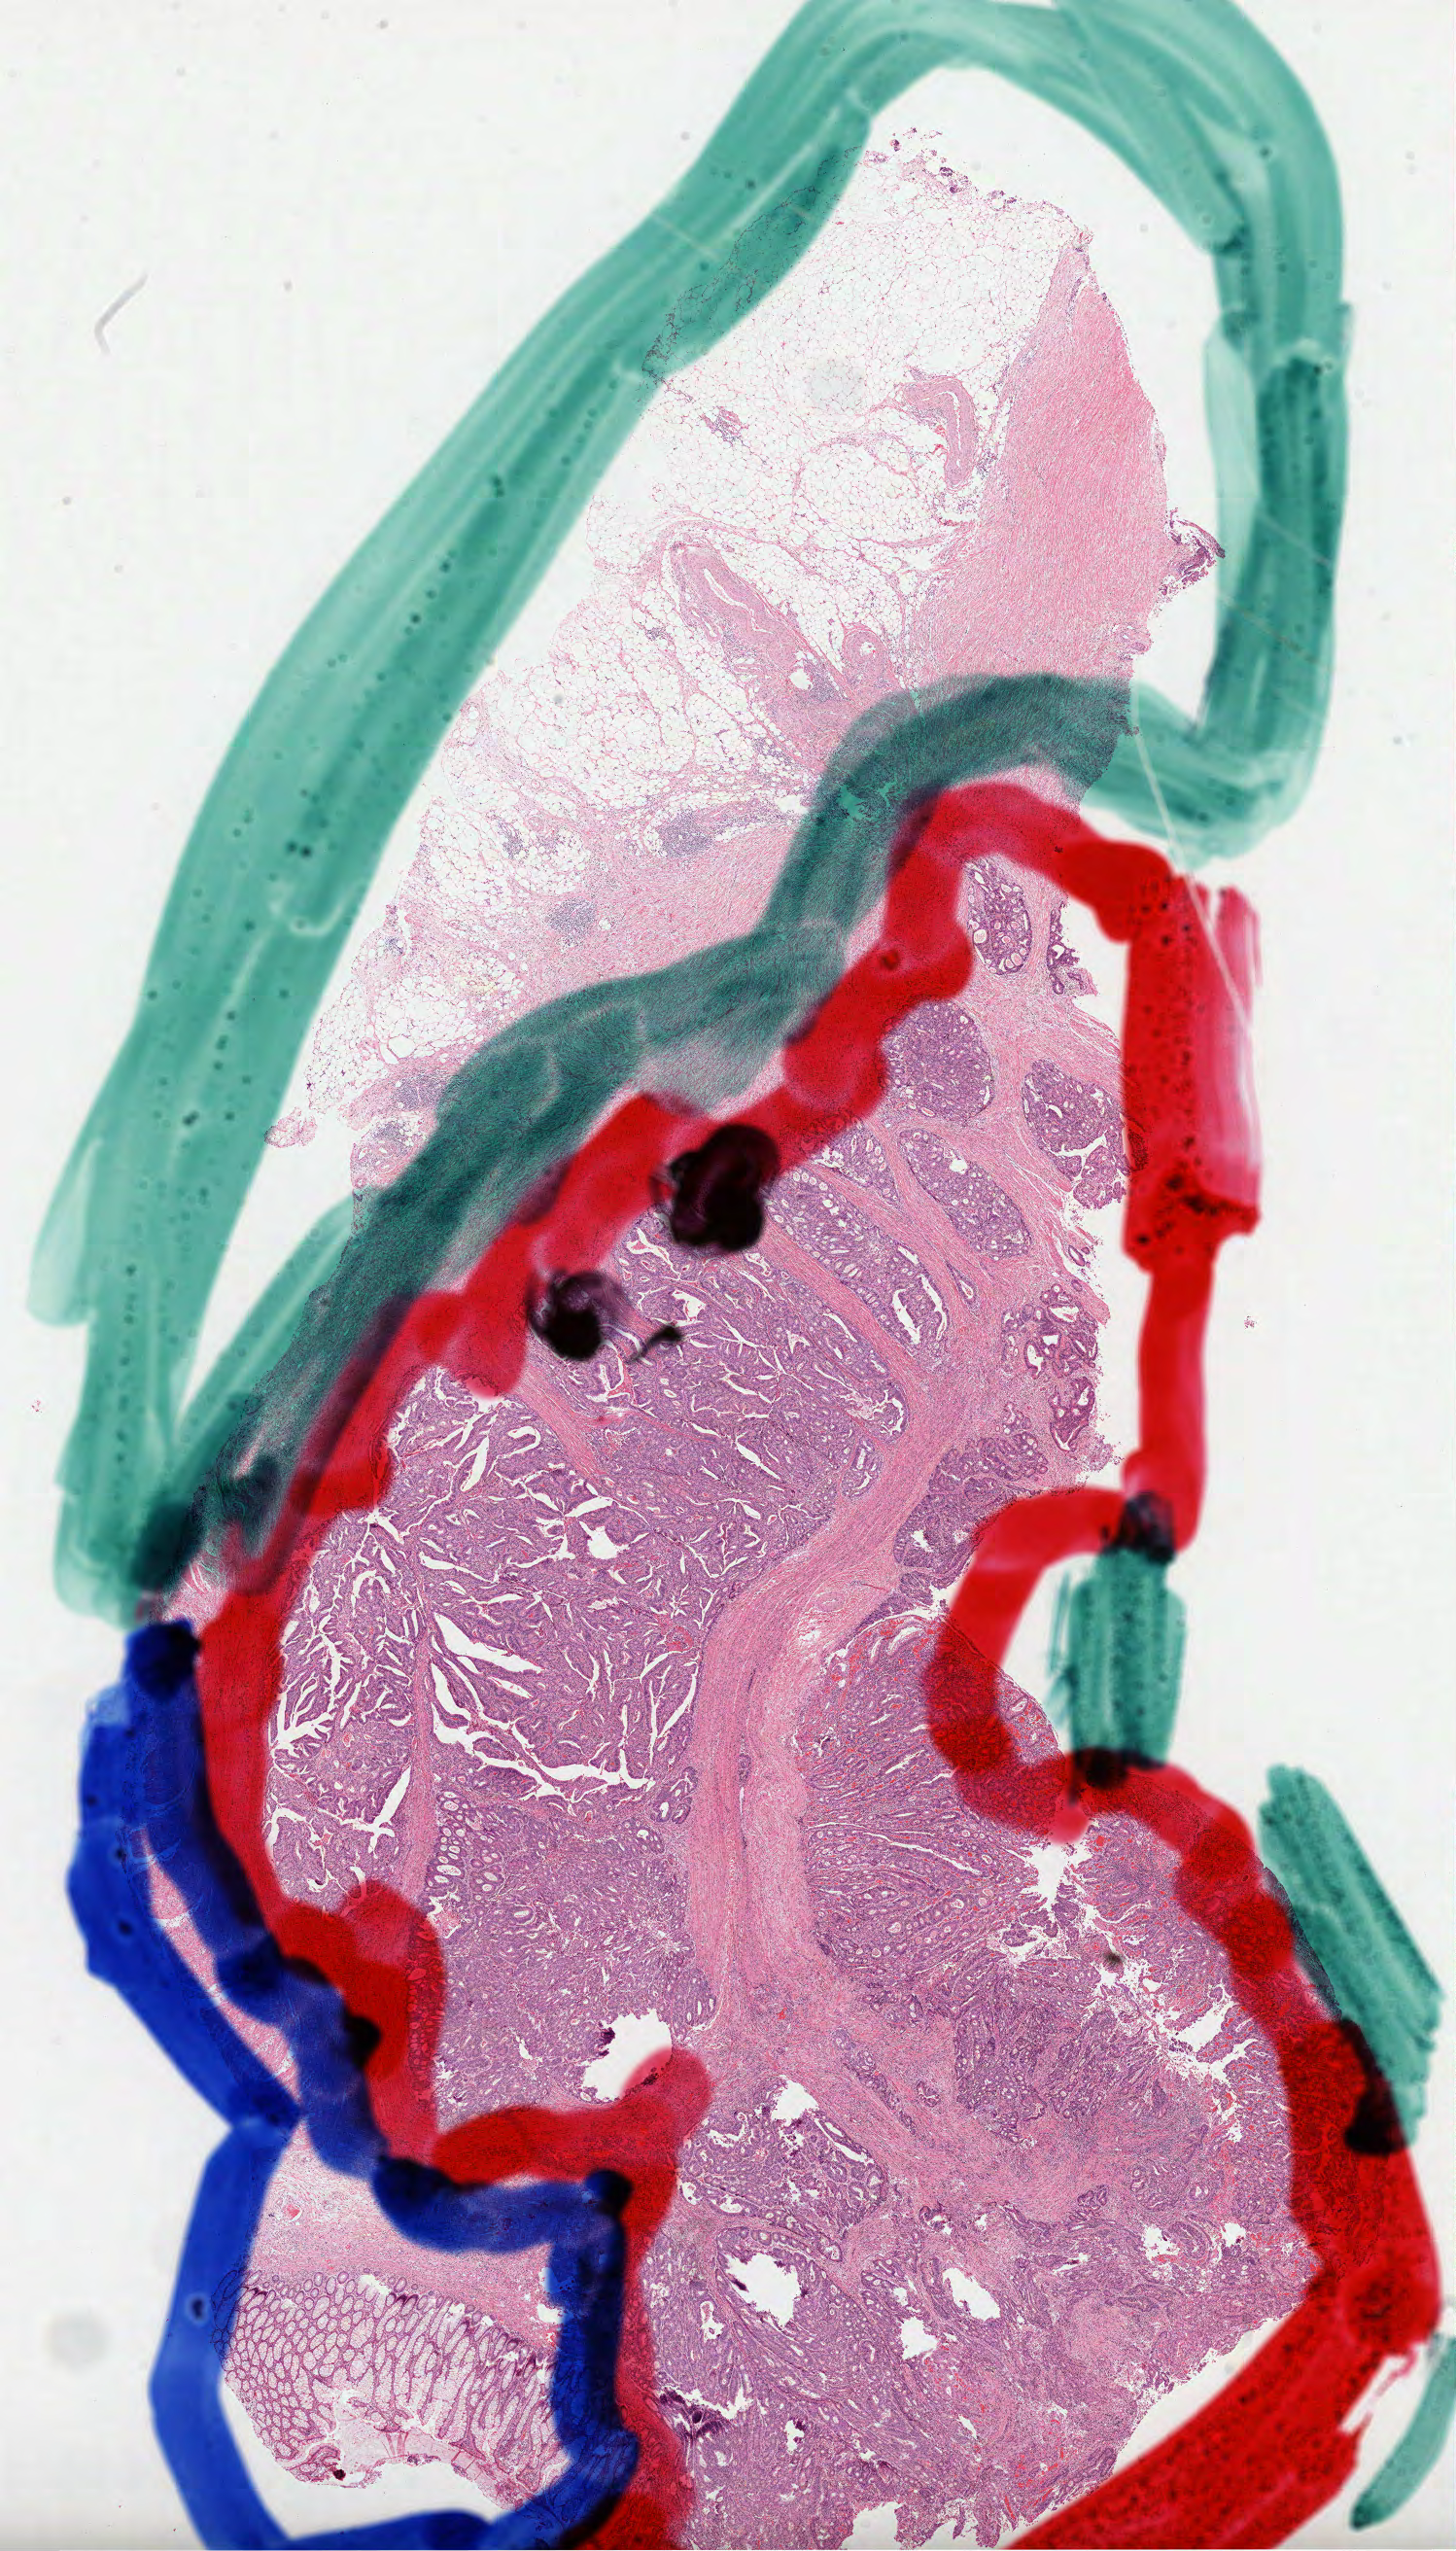
Whole-slide histology image, H&E-stained, whole scanned area (about 12.1 x 21.2 mm) shown as a low-resolution overview. Formalin-fixed paraffin-embedded (FFPE) diagnostic section. Colon, primary tumour sample. Female, age 77 years at initial diagnosis.
Diagnosis: Adenocarcinoma, NOS (sigmoid colon).